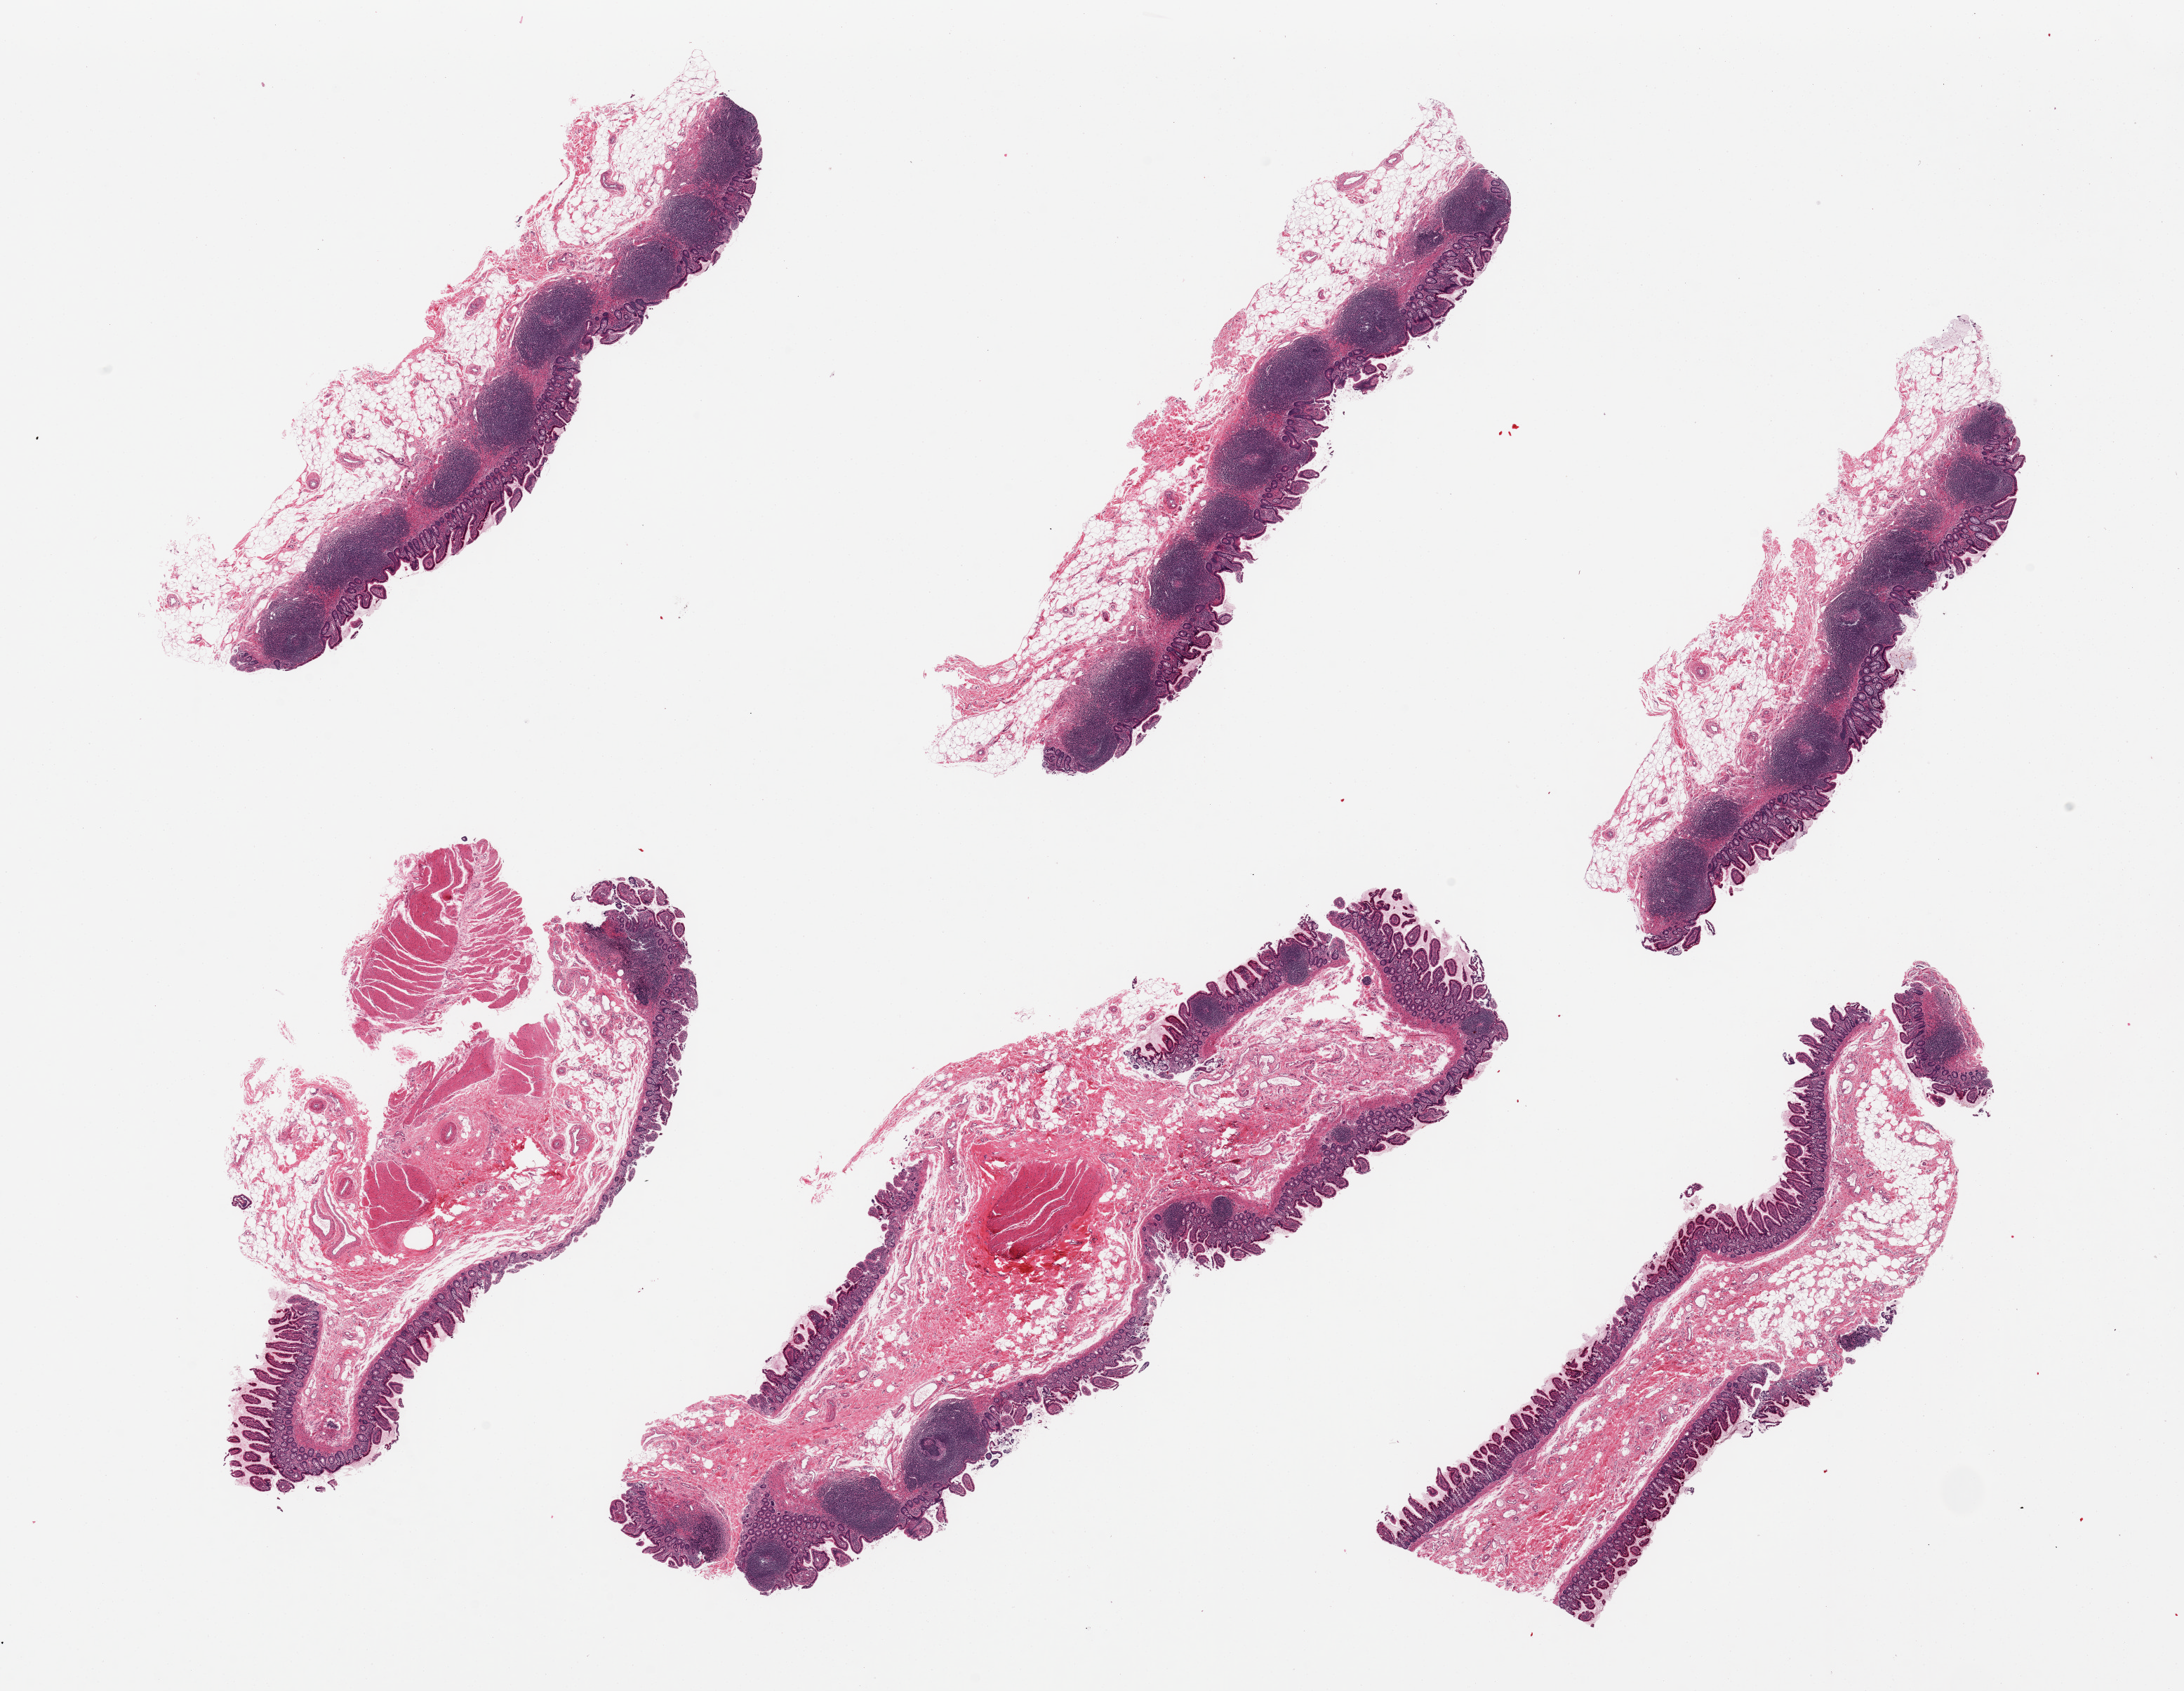
Hematoxylin and eosin (H&E) whole-slide image — low-resolution overview of the scanned area, about 24.6 x 19.1 mm, PAXgene-fixed paraffin-embedded (PFPE) section, sampled site (target tissue): ileum, tissue donor sample. Donor: male.
Reviewer comment on this tissue sample: 6 pieces, predominantly good specimens with good representation of lymphoid tissue. Small amount of muscularis included in 2.